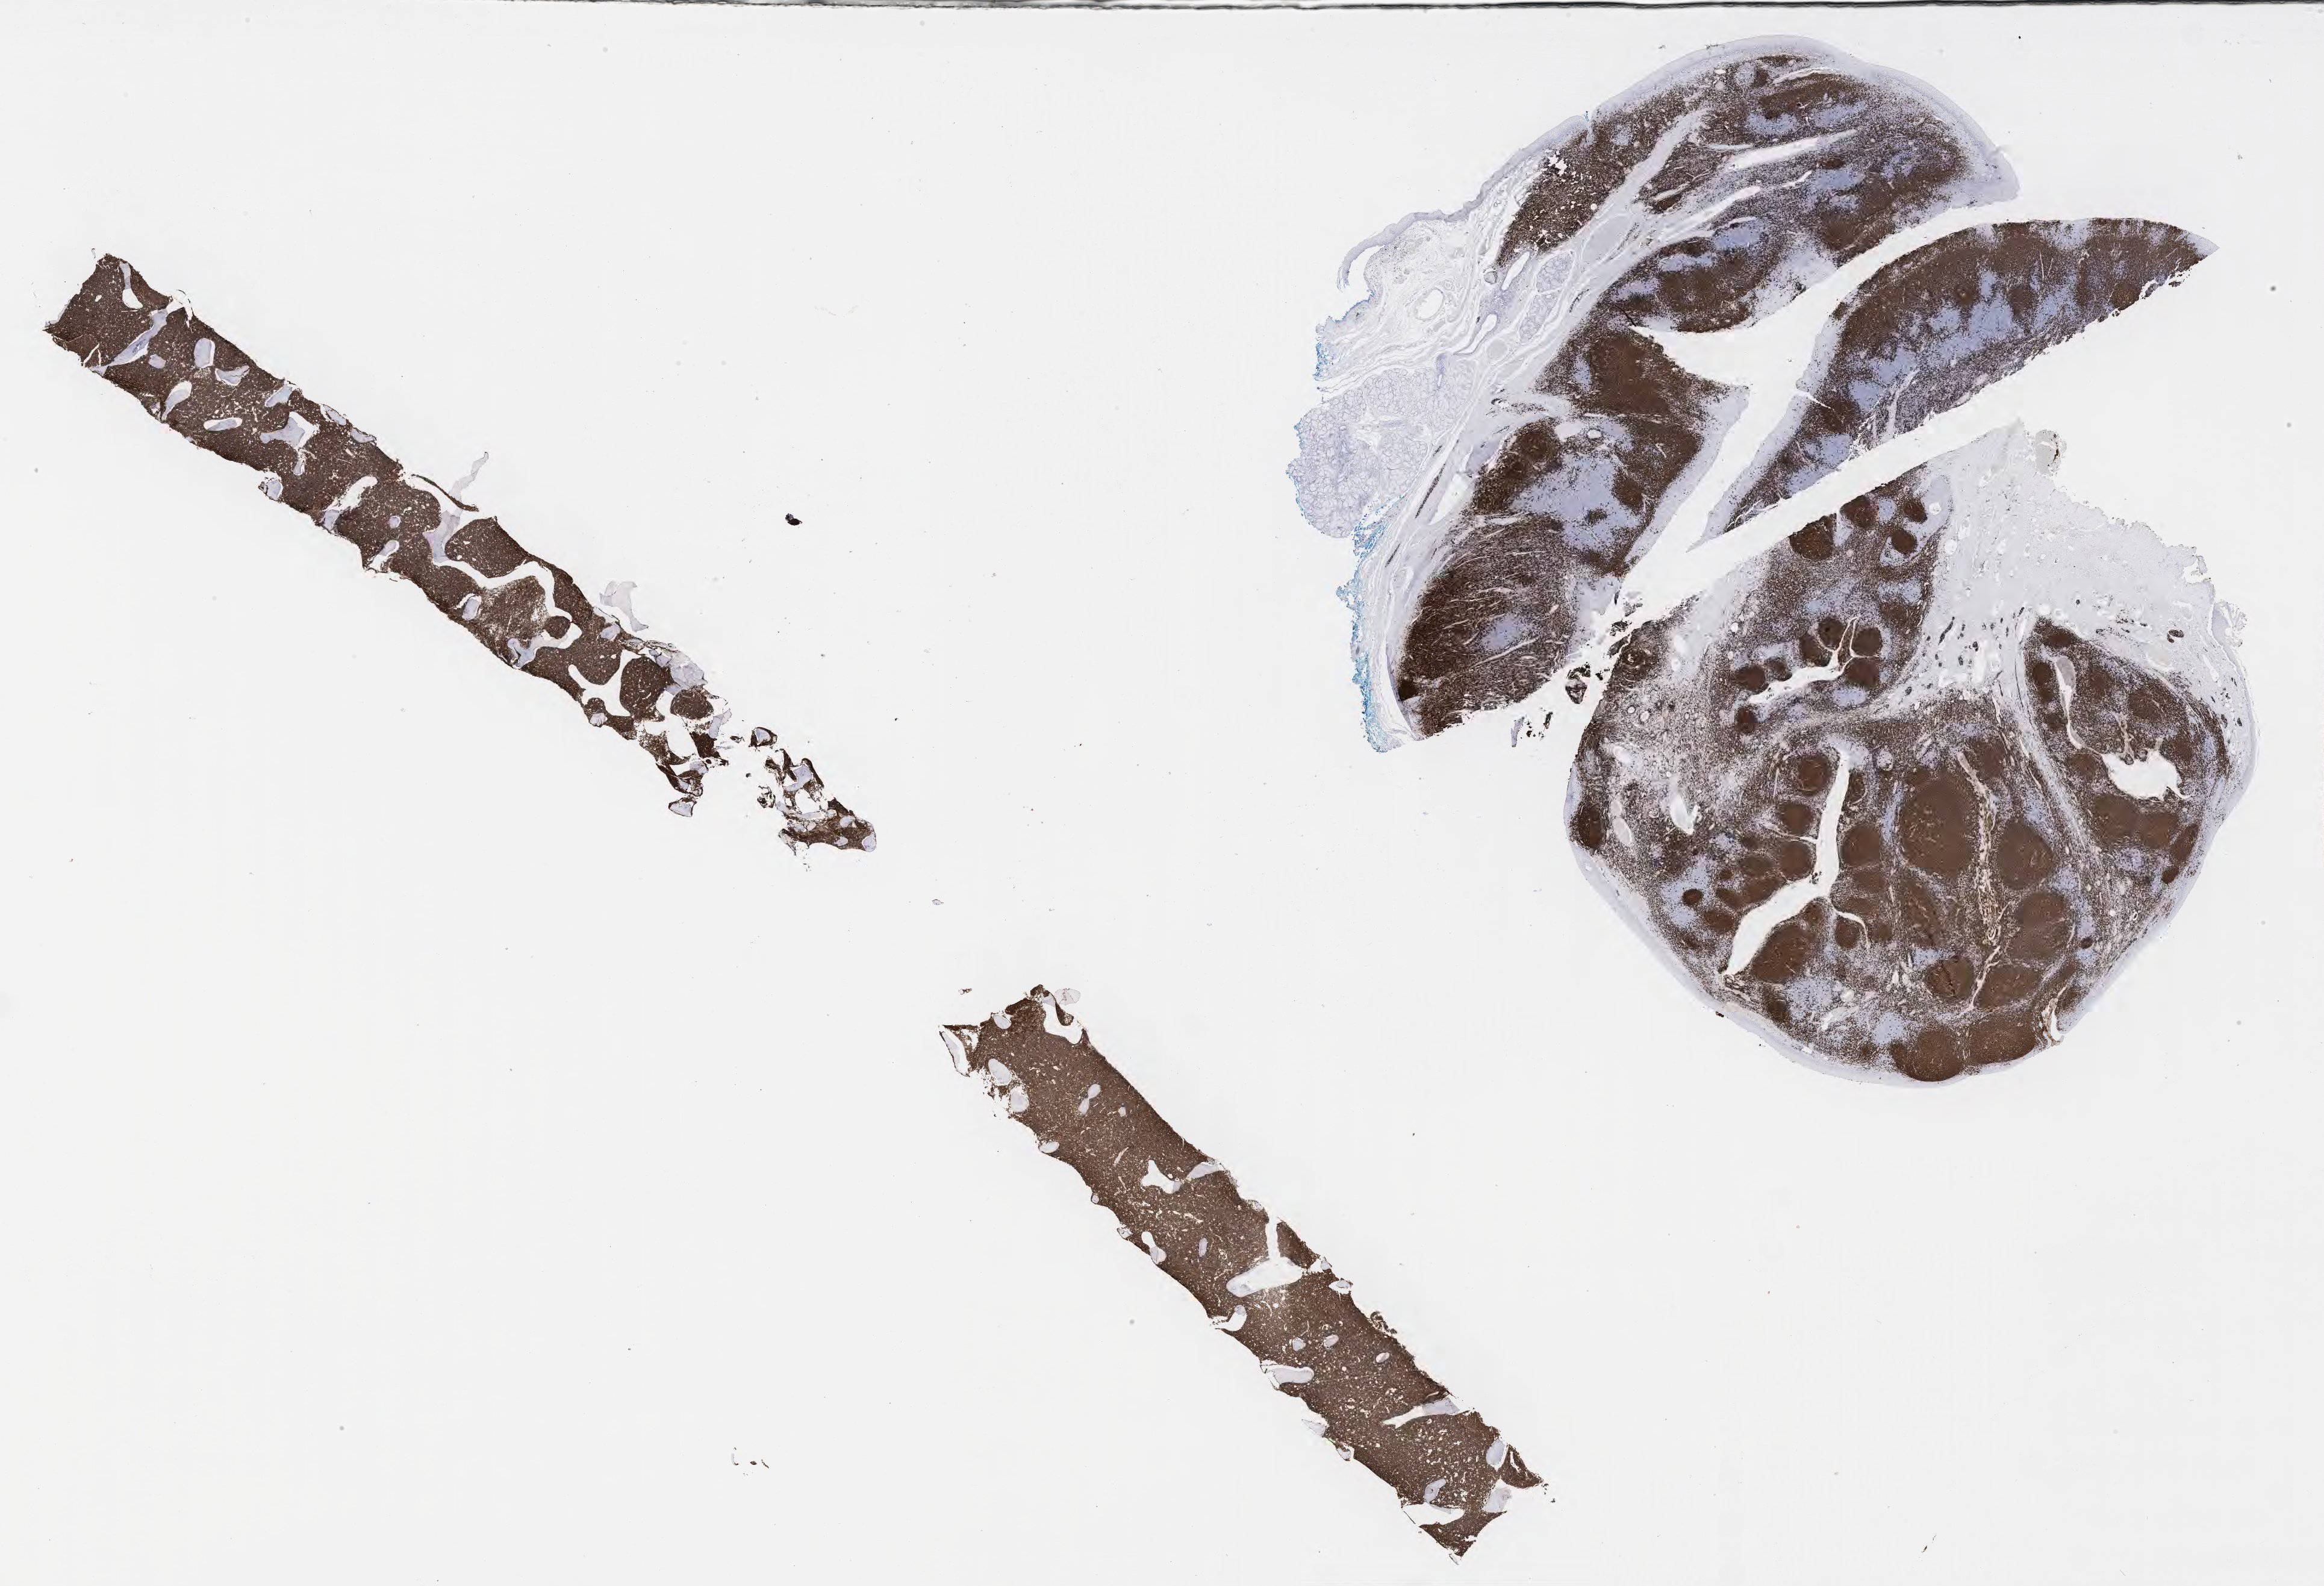
Immunohistochemistry (IHC) whole-slide image stained for CD20, a low-resolution overview of the entire scanned area, about 31.2 x 21.3 mm. Specimen: tumor tissue. Male, age 7 years at initial diagnosis.
Diagnosis: Burkitt lymphoma, NOS.